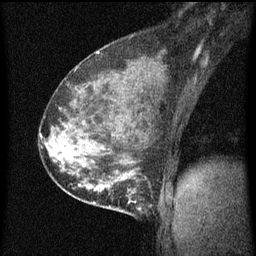
Breast MRI (dynamic contrast-enhanced), one sagittal slice. Position 37 of 60 along the scan axis. Dynamic contrast-enhanced series, image 2 of 3 at this slice position (ordered by acquisition). 1.5 T. TE 4.2 ms, TR 8 ms. 2 mm slice thickness. 256 × 256 image matrix, field of view 180 × 180 mm. Female patient, age 35 years.
Structures marked on this image (semi-automatic segmentation, software-assisted and operator-edited):
- analysis volume of interest (the breast-tissue region the enhancement analysis was run in; not a lesion): box from (x=110, y=178) to (x=155, y=219) px
- tumour enhancement mask (voxels above the 70 % enhancement threshold inside the analysis volume of interest): (x=110, y=178)–(x=142, y=211)